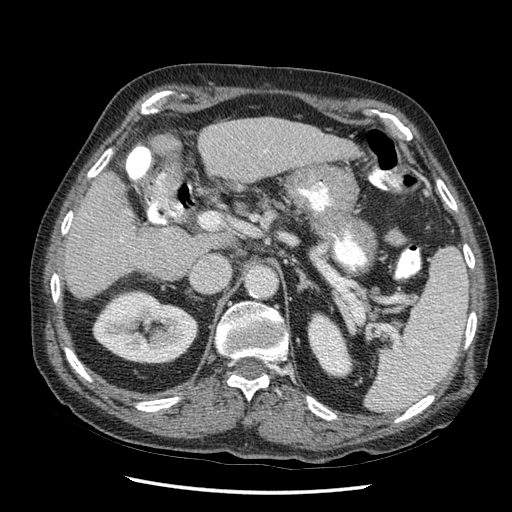
Contrast-enhanced abdominal CT (liver protocol), one axial slice; slice 22 of 67 in the series (ordered by position); reconstruction kernel STANDARD; soft-tissue window (W 400 / L 40 HU); 2.5 mm slice thickness; 512 × 512 image matrix. Case-level facts recorded for this patient, not image findings: diagnosis: hepatocellular carcinoma (patient treated with transarterial chemoembolisation; whether this scan precedes or follows treatment is not stated here); TNM stage (as recorded): Stage-I.
Outlined on this slice (semi-automatic segmentation, software-assisted and operator-edited):
- liver parenchyma outside the tumour (the mass and vessels are separate outlines, so this box may not span the whole liver): bounding box <64,118,354,296> (left, top, right, bottom; pixels)
- liver vessels: <105,143,242,246>